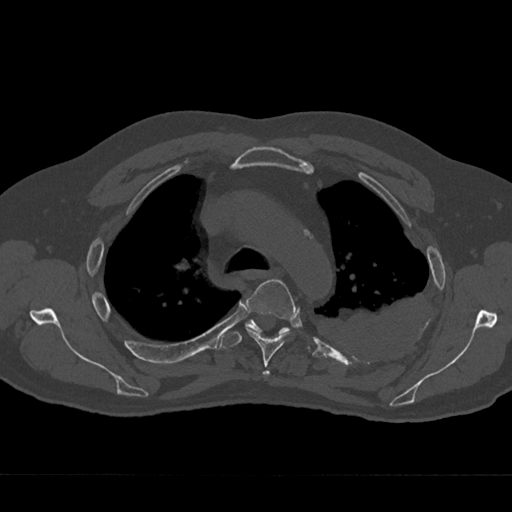
CT including the spine, one axial slice. Reconstruction kernel Br40s/3. Bone window (W 1800 / L 400 HU). 0.5 mm slice thickness. 512 × 512 image matrix, field of view 377 × 377 mm. Male patient, age 75 years. Case-level facts recorded for this patient, not image findings: primary cancer: renal.
Structures marked on this image (semi-automatic segmentation, software-assisted and operator-edited):
- T3 vertebra: bounding box (x1, y1, x2, y2) in pixels: (264, 371, 269, 374)
- T4 vertebra: (245, 279, 296, 376)
- T5 vertebra: (220, 320, 310, 349)